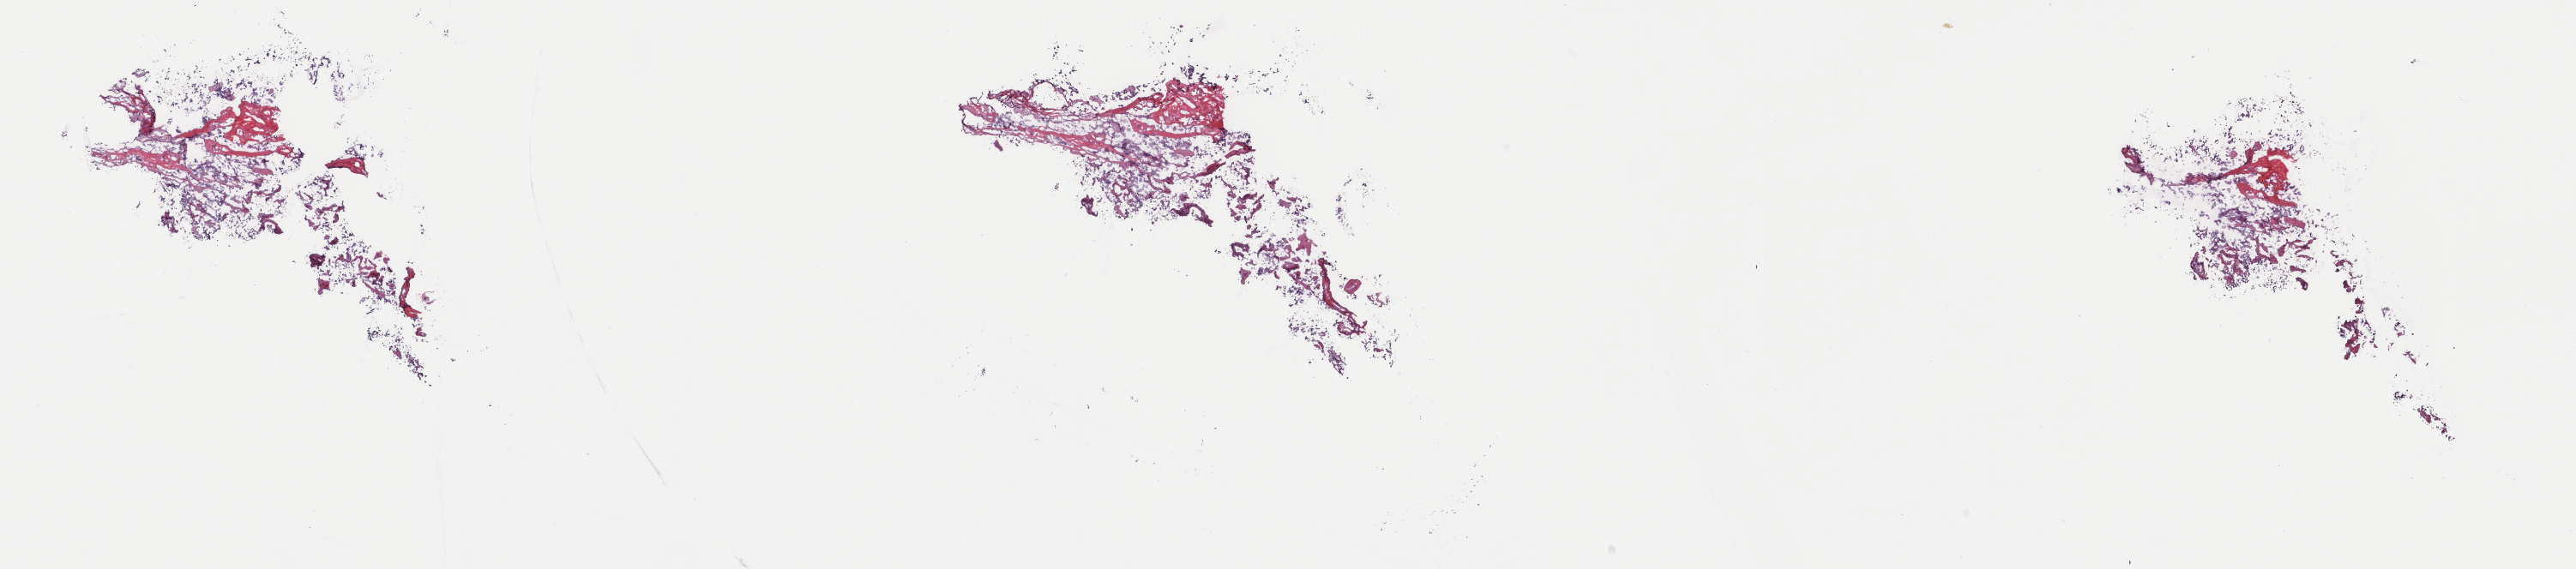
Whole-slide histology image, Hematoxylin and eosin (H&E) stained, low-resolution overview of the scanned area, about 23.8 x 5.3 mm (slide scanned at 40x), frozen section, sample: primary tumour, thyroid. Female, age 35 years at initial diagnosis. Slide review estimates, as recorded: tumour cells 40%, tumour nuclei 100%, normal cells 0%, stromal cells 60%, necrosis 0%. Inflammatory infiltration, as recorded: lymphocyte infiltration 0%, monocyte infiltration 2%, neutrophil infiltration 0%.
Diagnosis: Papillary adenocarcinoma, NOS (thyroid gland). Laterality: right. AJCC pathologic stage: I (7th edition).